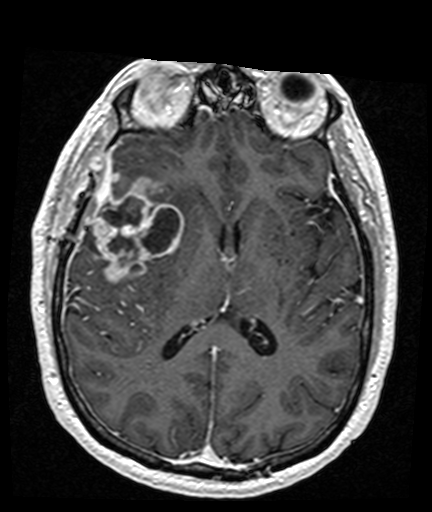
Brain MRI from a brain-tumour surgery series, one axial slice. Position 79 of 176 along the scan axis. T1-weighted post-contrast. 432 × 512 image matrix, field of view 194 × 230 mm. From the clinical record (not read from this slice): histopathology: Glioblastoma; WHO grade: 4; IDH mutation: no; tumour location: Right Frontal Temporal, Posterior Sylvian Fissure.
Structures marked on this image (expert manual segmentation):
- tumour: bounding box <93,176,183,284> (left, top, right, bottom; pixels)